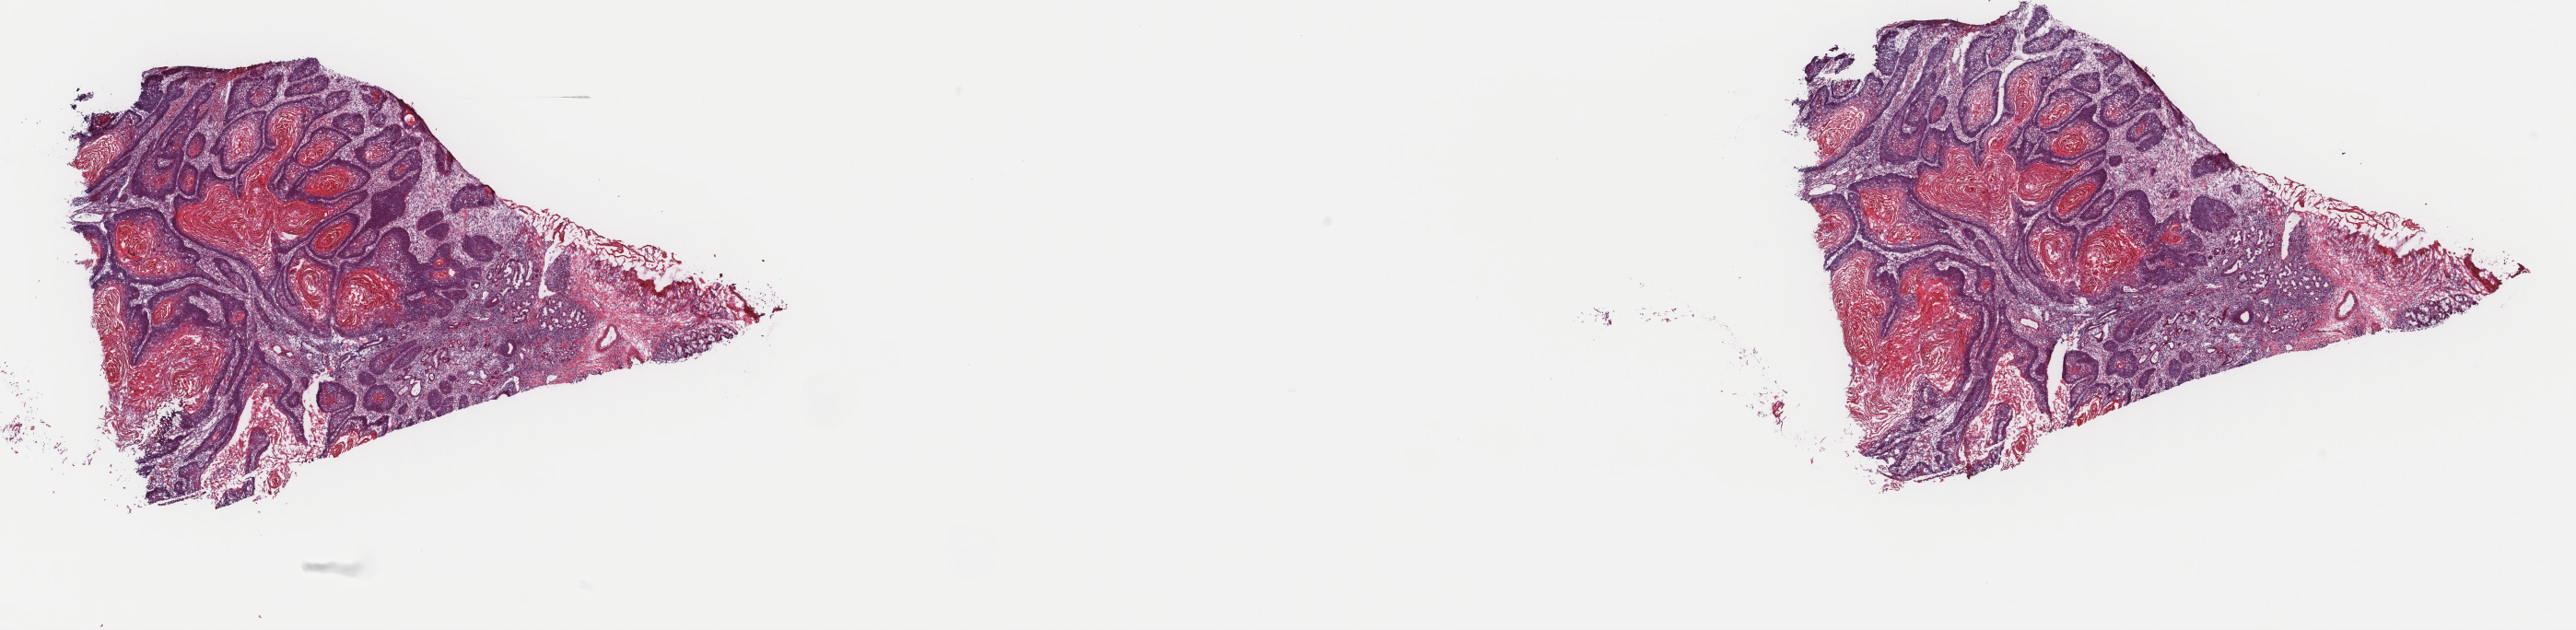
Digitized H&E tissue section (whole slide) — a low-resolution overview of the entire scanned area, about 22.2 x 5.4 mm (from a 40x scan); frozen section; sample: primary tumour, head and neck. Patient: male, age at initial diagnosis 54 years. Histologic grade: G1 (well differentiated). Composition of this section per pathologist review: tumour cells 65%, tumour nuclei 90%, normal cells 10%, stromal cells 25%, necrosis 0%. Inflammatory infiltration, as recorded: lymphocyte infiltration 8%, monocyte infiltration 1%, neutrophil infiltration 0%.
• diagnosis: Squamous cell carcinoma, NOS (base of tongue, NOS)
• AJCC pathologic stage: II (7th edition)